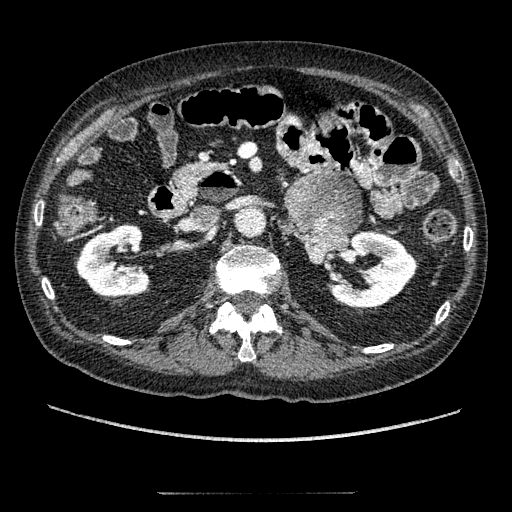
Contrast-enhanced abdominal CT, one axial slice. Position 97 of 274 along the scan axis. Intravenous contrast given. Soft-tissue window (W 400 / L 40 HU). 512 × 512 image matrix, field of view 381 × 381 mm. Male patient, age 69 years. From the clinical record (not read from this slice): diagnosis: adrenocortical carcinoma; tumour side: left adrenal; tumour size at pathology: 6.1 cm; Ki-67 index: 10 %; stage (as recorded): 3.
Structures marked on this image (semi-automatically segmented with operator editing):
- mass: bounding box <285,174,361,263> (left, top, right, bottom; pixels)